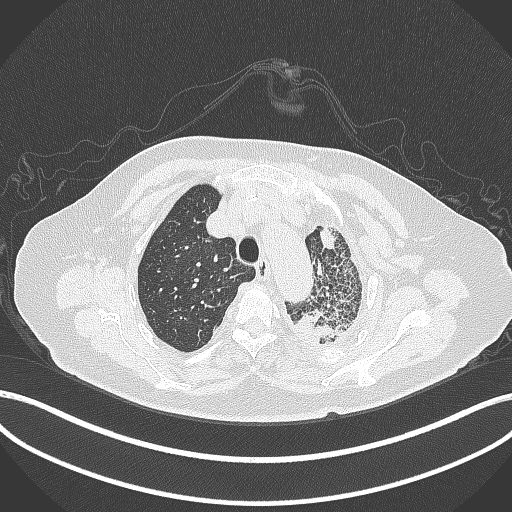
Chest CT, one axial slice; reconstruction kernel B70f; 120 kVp; lung window (W 1500 / L -600 HU); 1 mm slice thickness; 512 × 512 image matrix, field of view 400 × 400 mm. Female patient, age 75 years. Case-level facts recorded for this patient, not image findings: clinical TNM (as recorded): T3 N3 M1.
Outlined on this slice (bounding box drawn by a radiologist):
- lung tumour (recorded histology: adenocarcinoma): bounding box [x1, y1, x2, y2] px = [295, 305, 353, 350]